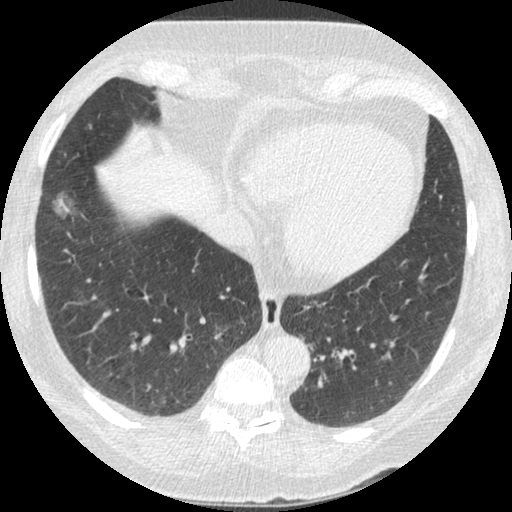
Low-dose screening chest CT, one axial slice; slice 89 of 245 in the series (ordered by position); 120 kVp; lung window (W 1500 / L -600 HU); 1.25 mm slice thickness; 512 × 512 image matrix, field of view 310 × 310 mm.
Structures marked on this image (expert manual segmentation):
- lesion 1 (tumor, lower lobe of right lung): box from (x=52, y=192) to (x=73, y=219) px